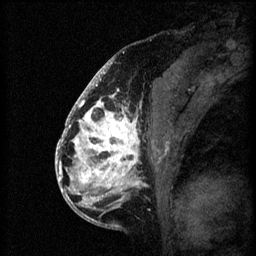
Breast MRI (dynamic contrast-enhanced), one sagittal slice. Slice 33 of 60 in the series (ordered by position). 3 images stored at this slice position (order not interpretable as contrast timing). 1.5 T. TE 4.2 ms, TR 8.2 ms. 2 mm slice thickness. 256 × 256 image matrix, field of view 180 × 180 mm. Patient: female, 41 years.
Annotated regions visible in this slice (semi-automatic segmentation, software-assisted and operator-edited):
- analysis volume of interest (the breast-tissue region the enhancement analysis was run in; not a lesion): box from (x=72, y=108) to (x=167, y=205) px
- tumour enhancement mask (voxels above the 70 % enhancement threshold inside the analysis volume of interest): (x=72, y=108)–(x=142, y=205)